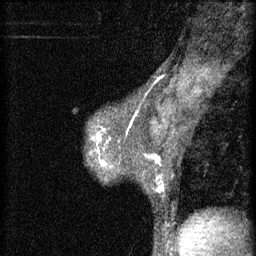
Breast MRI (dynamic contrast-enhanced), one sagittal slice; slice 40 of 60 in the series (ordered by position); 3 images stored at this slice position (order not interpretable as contrast timing); 1.5 T; TE 4.2 ms, TR 11 ms; 2 mm slice thickness; 256 × 256 image matrix, field of view 180 × 180 mm. Female patient, age 37 years.
Structures marked on this image (semi-automatically segmented with operator editing):
- analysis volume of interest (the breast-tissue region the enhancement analysis was run in; not a lesion): bounding box (x1, y1, x2, y2) in pixels: (90, 138, 162, 193)
- tumour enhancement mask (voxels above the 70 % enhancement threshold inside the analysis volume of interest): (97, 140, 160, 193)